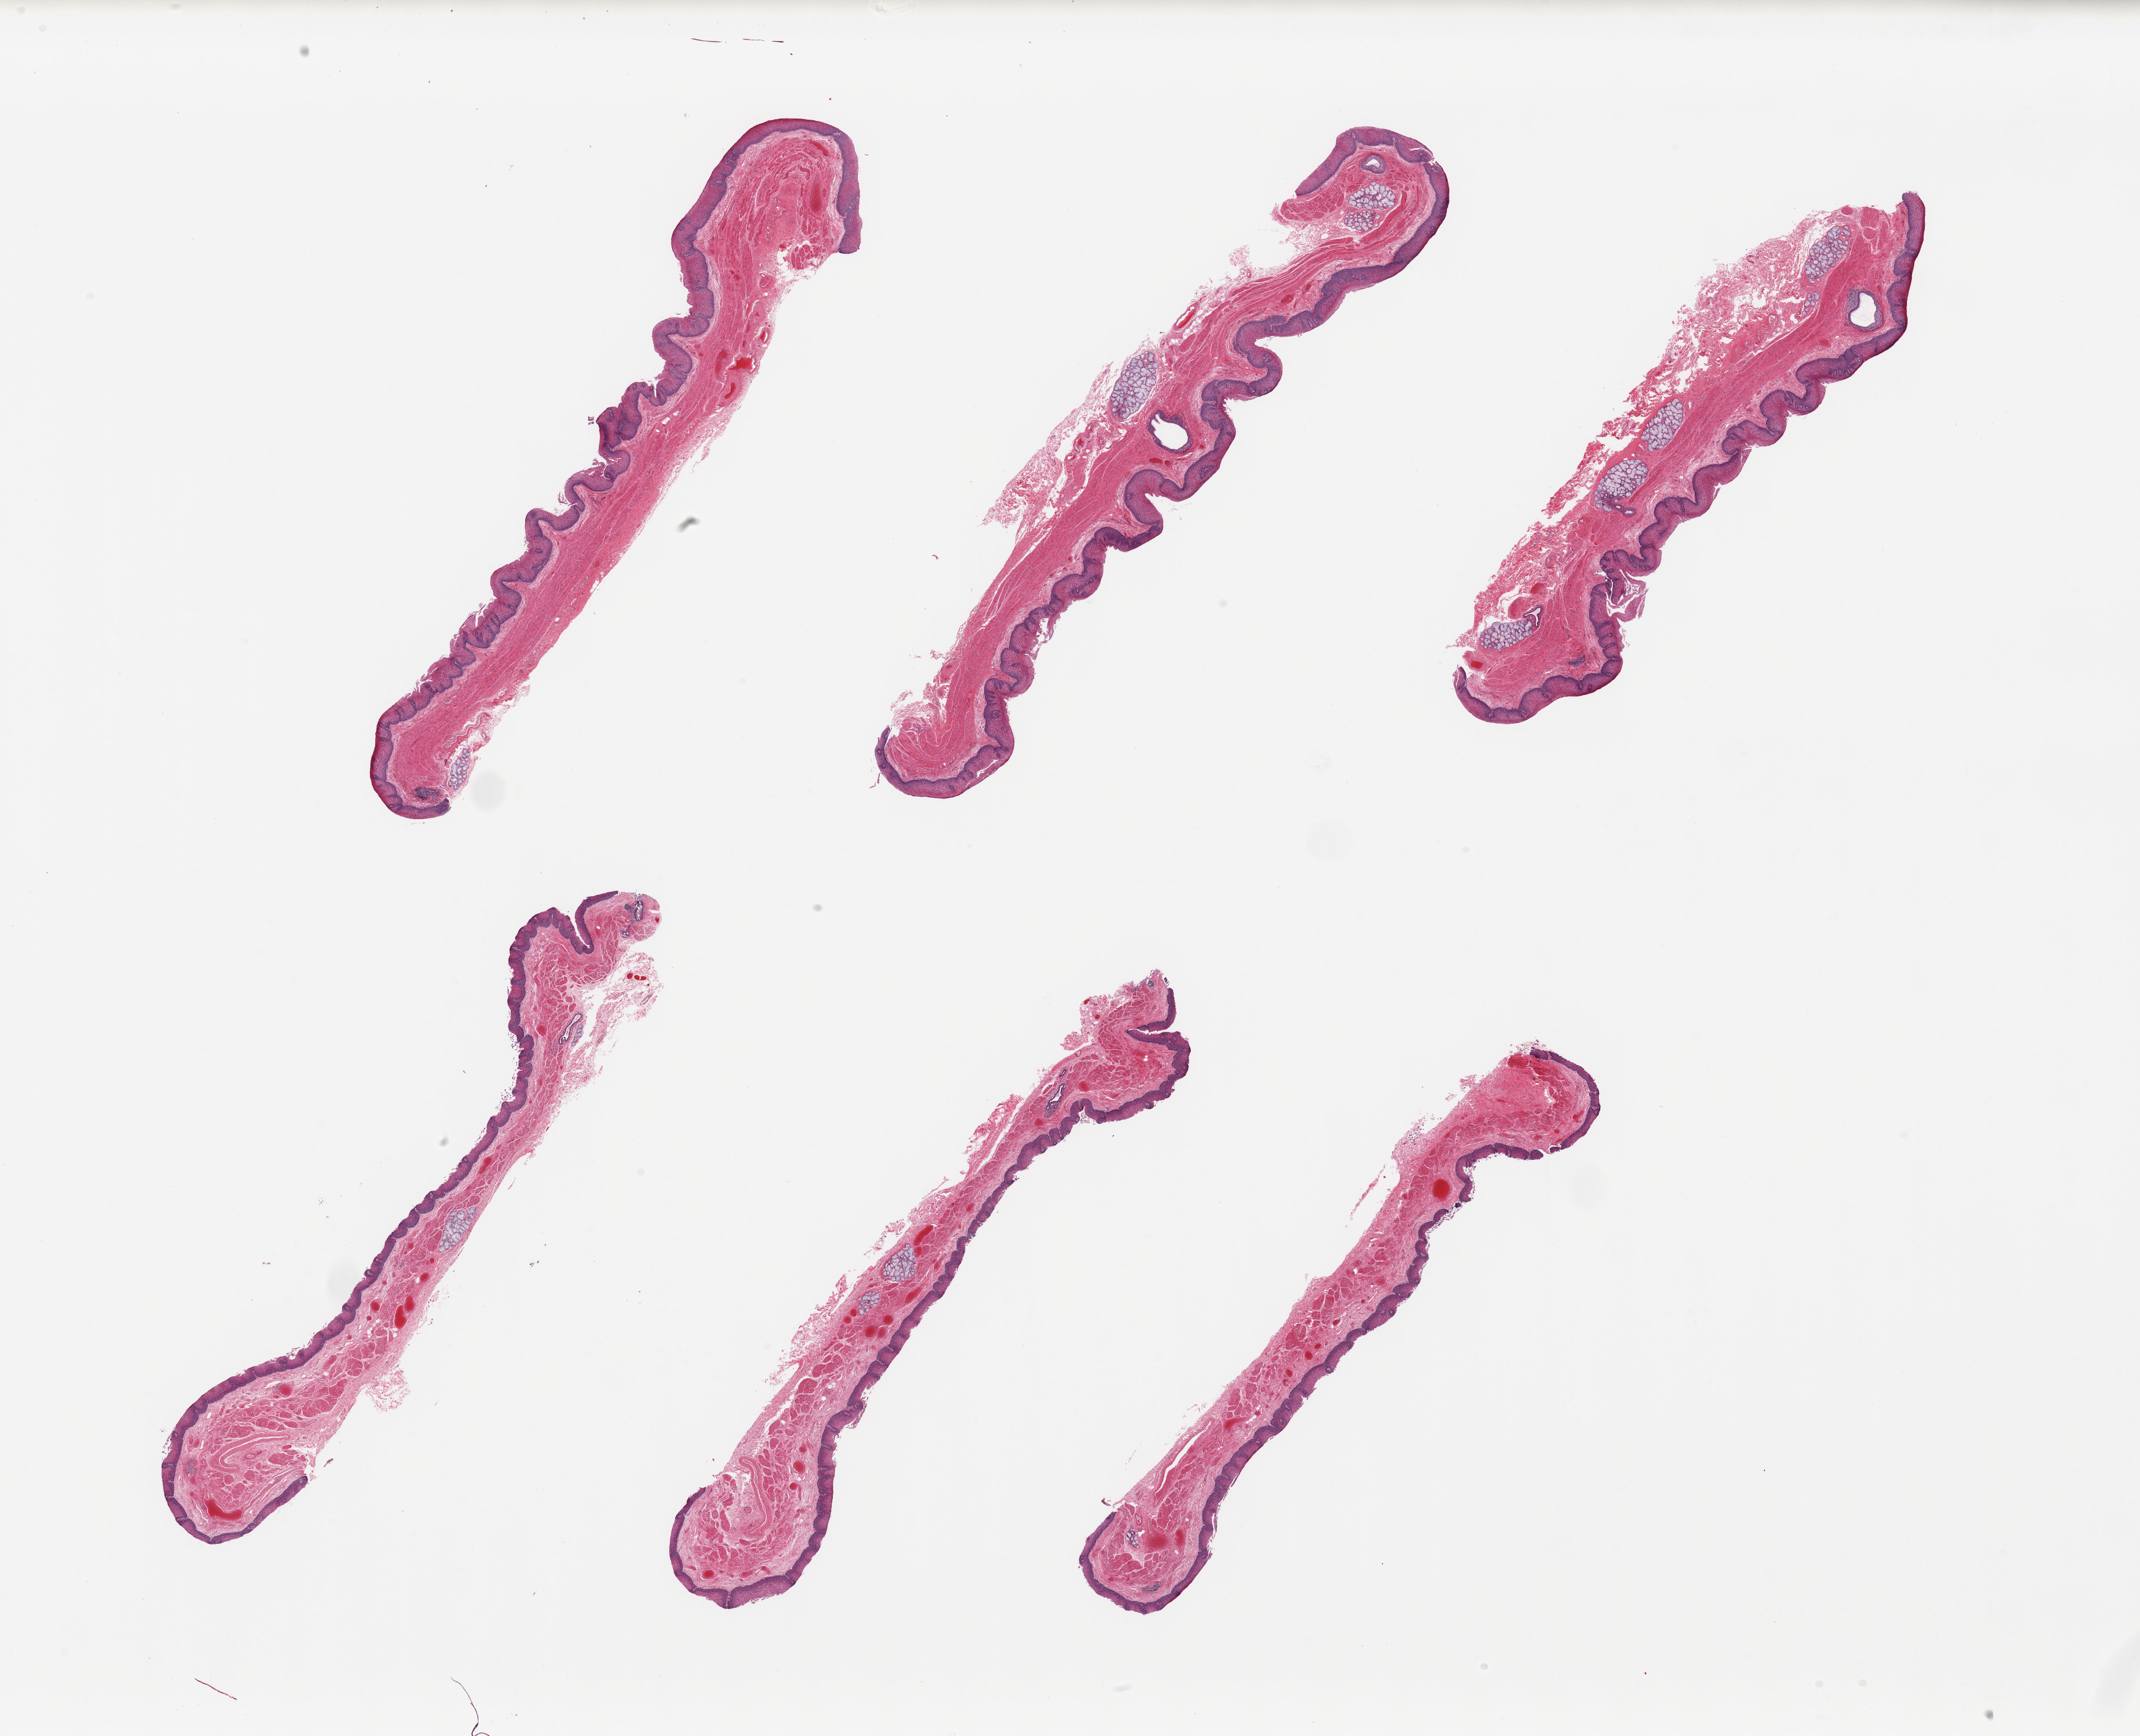
Hematoxylin and eosin (H&E) whole-slide image, brightfield — a low-resolution overview of the entire scanned area, about 28.5 x 23.2 mm. PAXgene-fixed, paraffin-embedded tissue. Sampled site (target tissue): esophageal mucous membrane. Donor tissue sample. Male donor.
- reviewer comment on this tissue sample: 6 pieces; several prominent submucosal glands with dilated chronically inflamed ducts